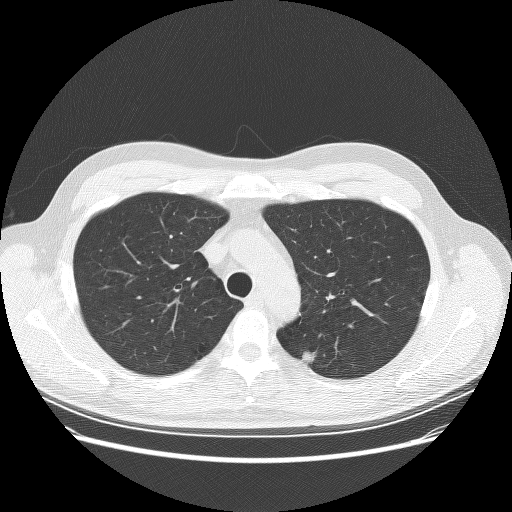
Low-dose screening chest CT, one axial slice. Slice 200 of 253 in the series (ordered by position). Reconstruction kernel BONE. Lung window (W 1500 / L -600 HU). 512 × 512 image matrix, field of view 370 × 370 mm.
Annotated regions visible in this slice (expert manual segmentation):
- lesion 2 (nodule): box from (x=303, y=351) to (x=317, y=363) px